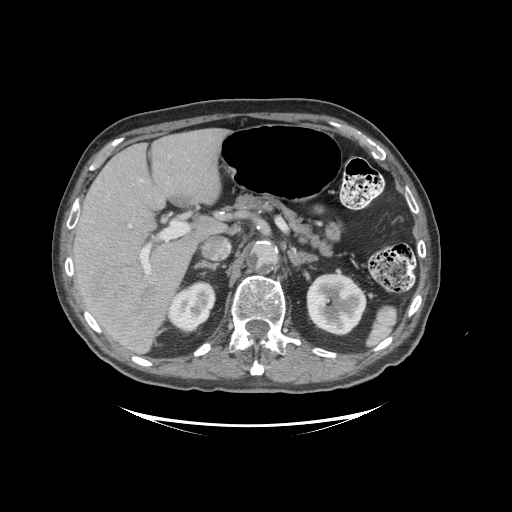
Contrast-enhanced abdominal CT (liver protocol), one axial slice. Position 60 of 99 along the scan axis. Soft-tissue window (W 400 / L 40 HU). 2.5 mm slice thickness. 512 × 512 image matrix. Case-level facts recorded for this patient, not image findings: diagnosis: hepatocellular carcinoma (patient treated with transarterial chemoembolisation; whether this scan precedes or follows treatment is not stated here); TNM stage (as recorded): Stage-I; Child-Pugh class: A.
Annotated regions visible in this slice (semi-automatically segmented with operator editing):
- liver parenchyma outside the tumour (the mass and vessels are separate outlines, so this box may not span the whole liver): bounding box <72,128,228,352> (left, top, right, bottom; pixels)
- mass: <78,259,176,346>
- liver vessels: <128,180,189,274>